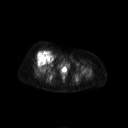
FDG PET of an extremity soft-tissue mass (from a PET/CT study), one axial slice. Position 61 of 267 along the scan axis. 128 × 128 image matrix. Patient: female, 56 years. From the clinical record (not read from this slice): histological type: malignant solitary fibrous tumor; grade: intermediate; site of the primary tumour: right thigh.
Annotated regions visible in this slice (expert contour drawn on MRI and transferred to this co-registered scan by the dataset authors):
- gross tumour volume including surrounding oedema: bounding box (x1, y1, x2, y2) in pixels: (36, 50, 50, 62)
- gross tumour volume (mass): (36, 51, 50, 61)